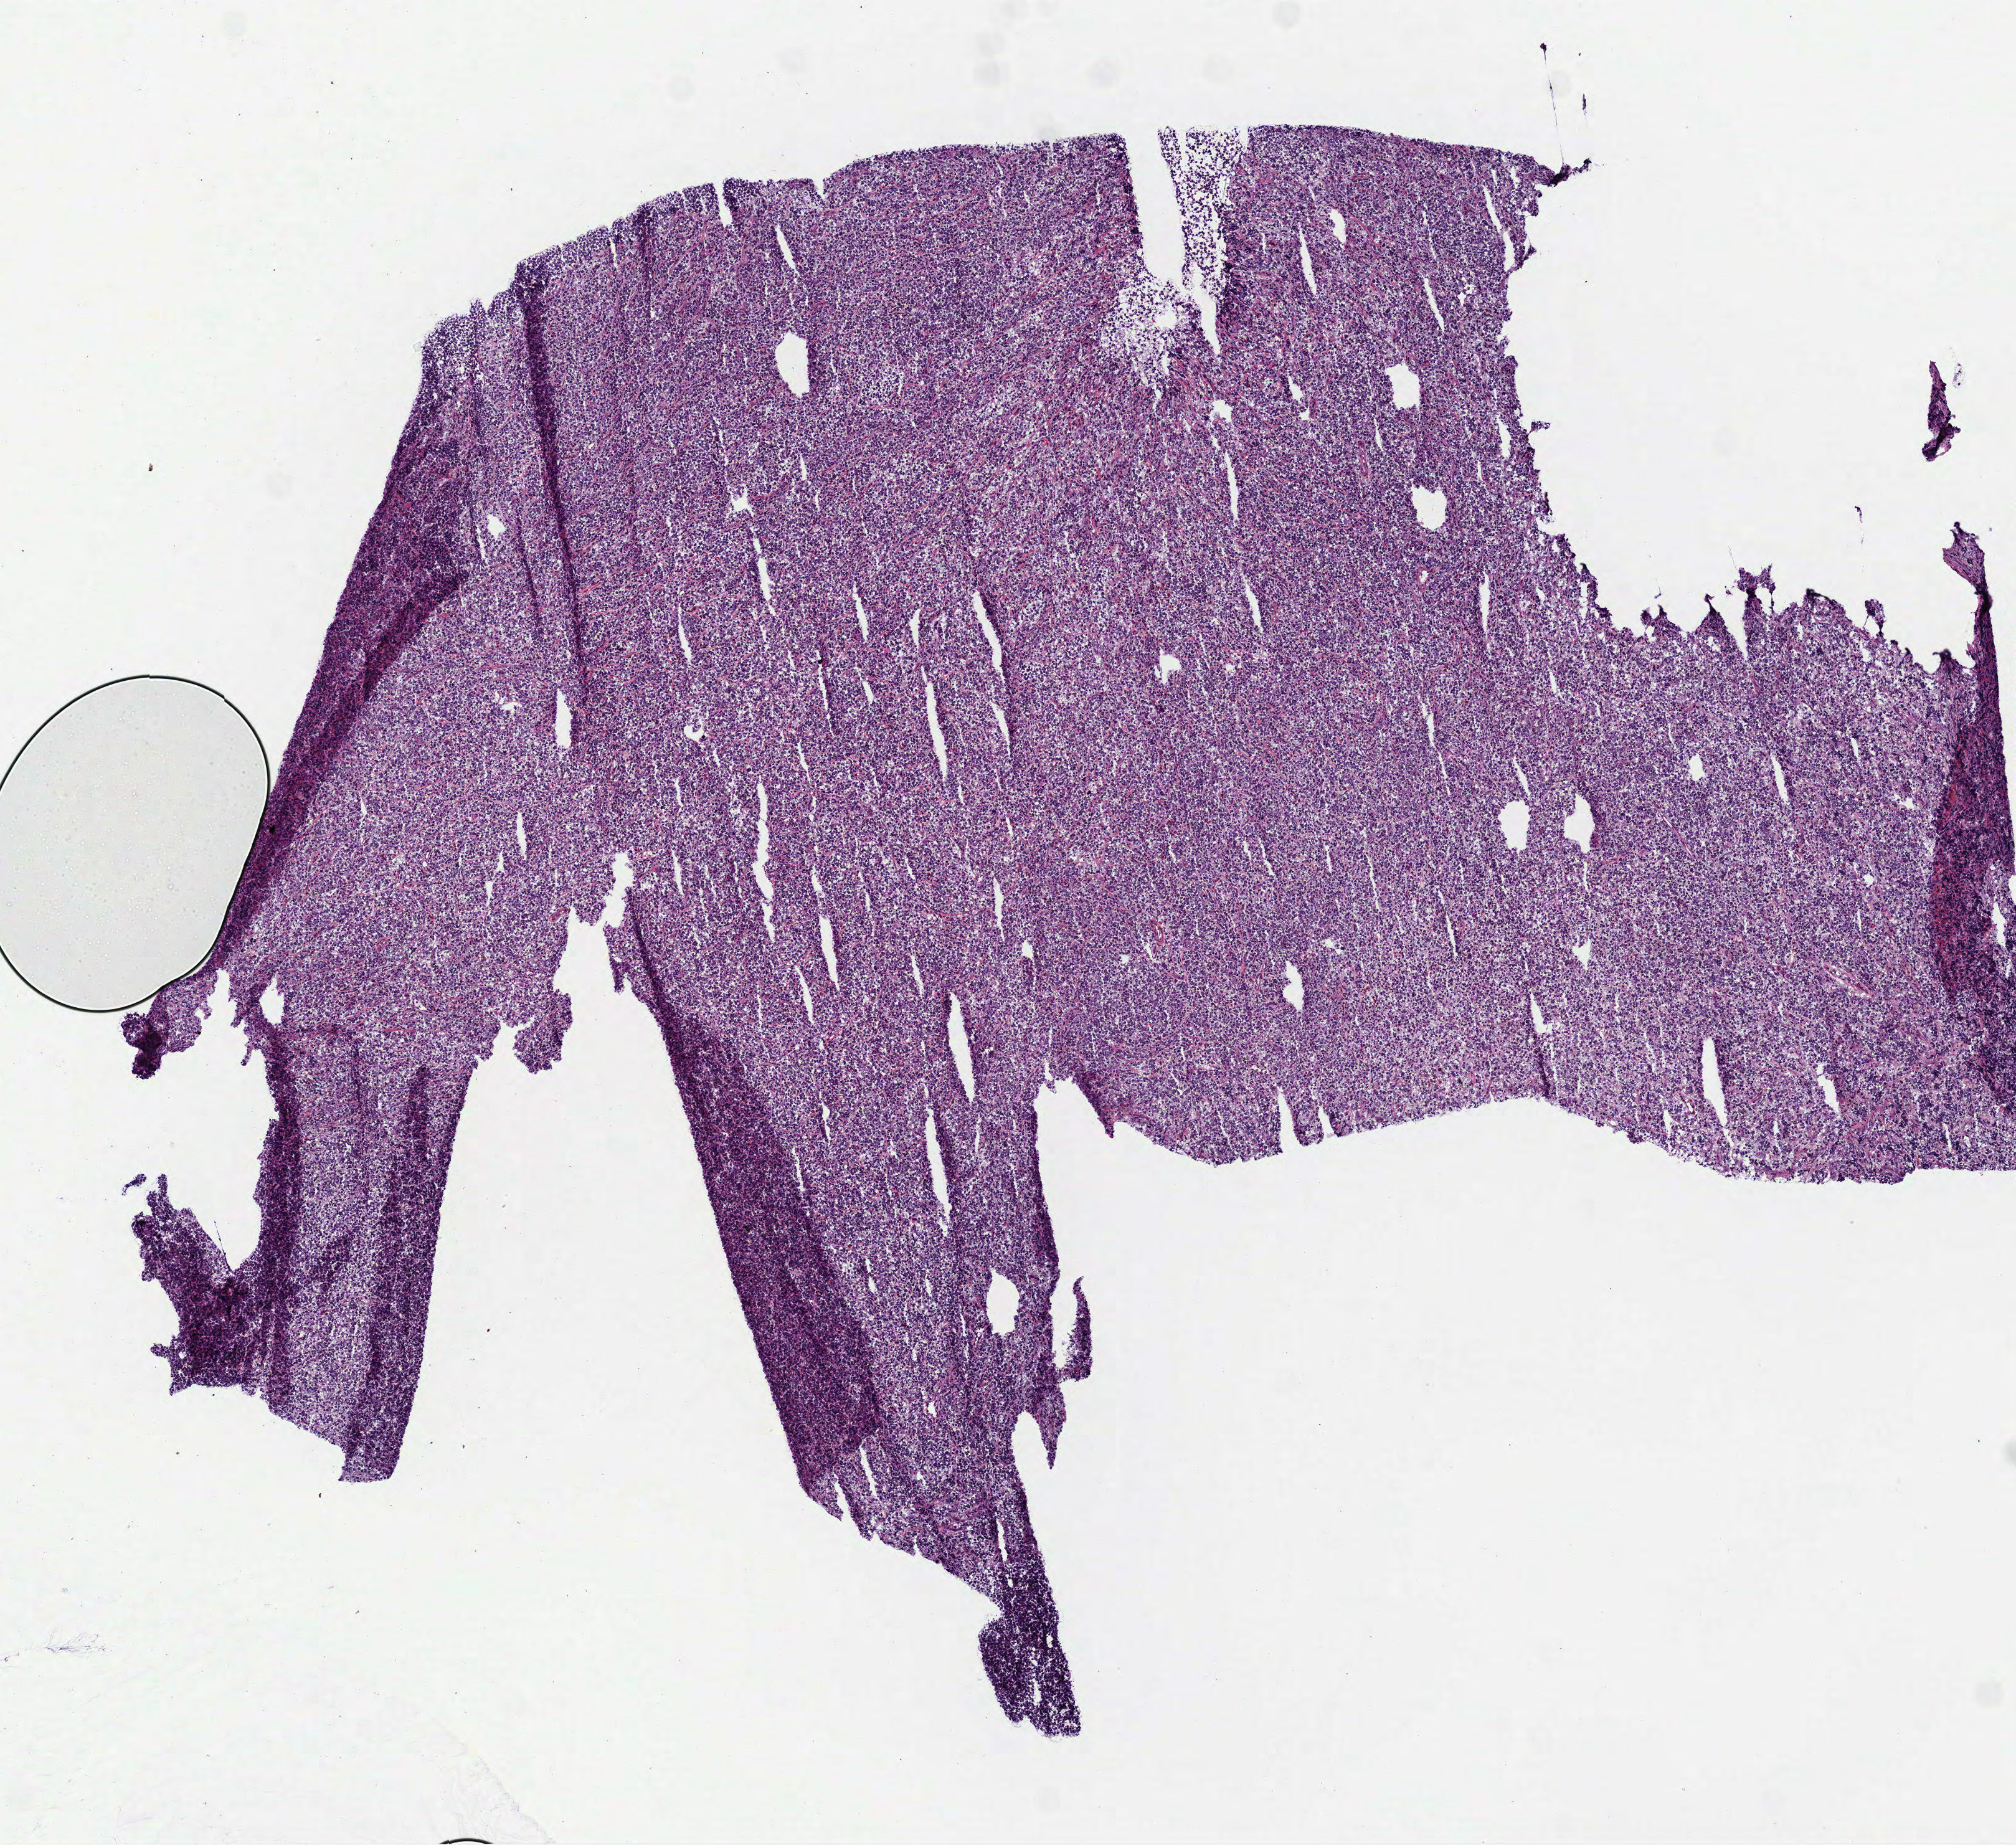
Digitized Hematoxylin and eosin (H&E) stained tissue section (whole slide), shown as a low-resolution overview of the whole scanned area (about 6.5 x 6.0 mm); frozen section; lymphoid tissue, primary tumour sample. Patient: female, age at initial diagnosis 70 years. Pathologist review of this section (percent, as recorded): tumour cells 100%, tumour nuclei 88%, normal cells 0%, stromal cells 0%, necrosis 0%. Inflammatory infiltration, as recorded: lymphocyte infiltration 9%, monocyte infiltration 0%, neutrophil infiltration 2%.
Diagnosis: Diffuse large B-cell lymphoma, NOS (colon, NOS).